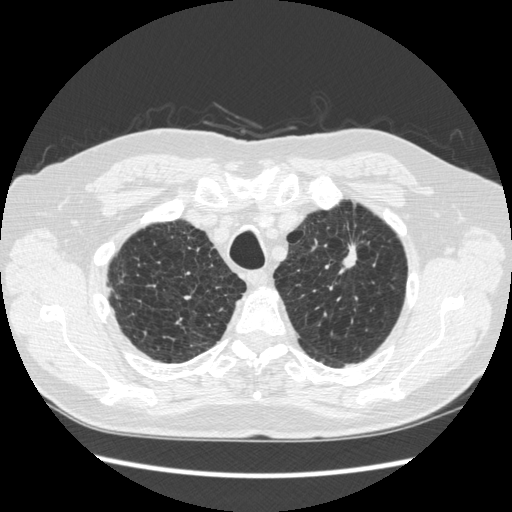
Low-dose screening chest CT, one axial slice. Slice 226 of 267 in the series (ordered by position). 120 kVp. Lung window (W 1500 / L -600 HU). 512 × 512 image matrix, field of view 360 × 360 mm.
Annotated regions visible in this slice (manually delineated by an expert):
- lesion 1 (tumor, upper lobe of left lung): bounding box <341,244,357,273> (left, top, right, bottom; pixels)